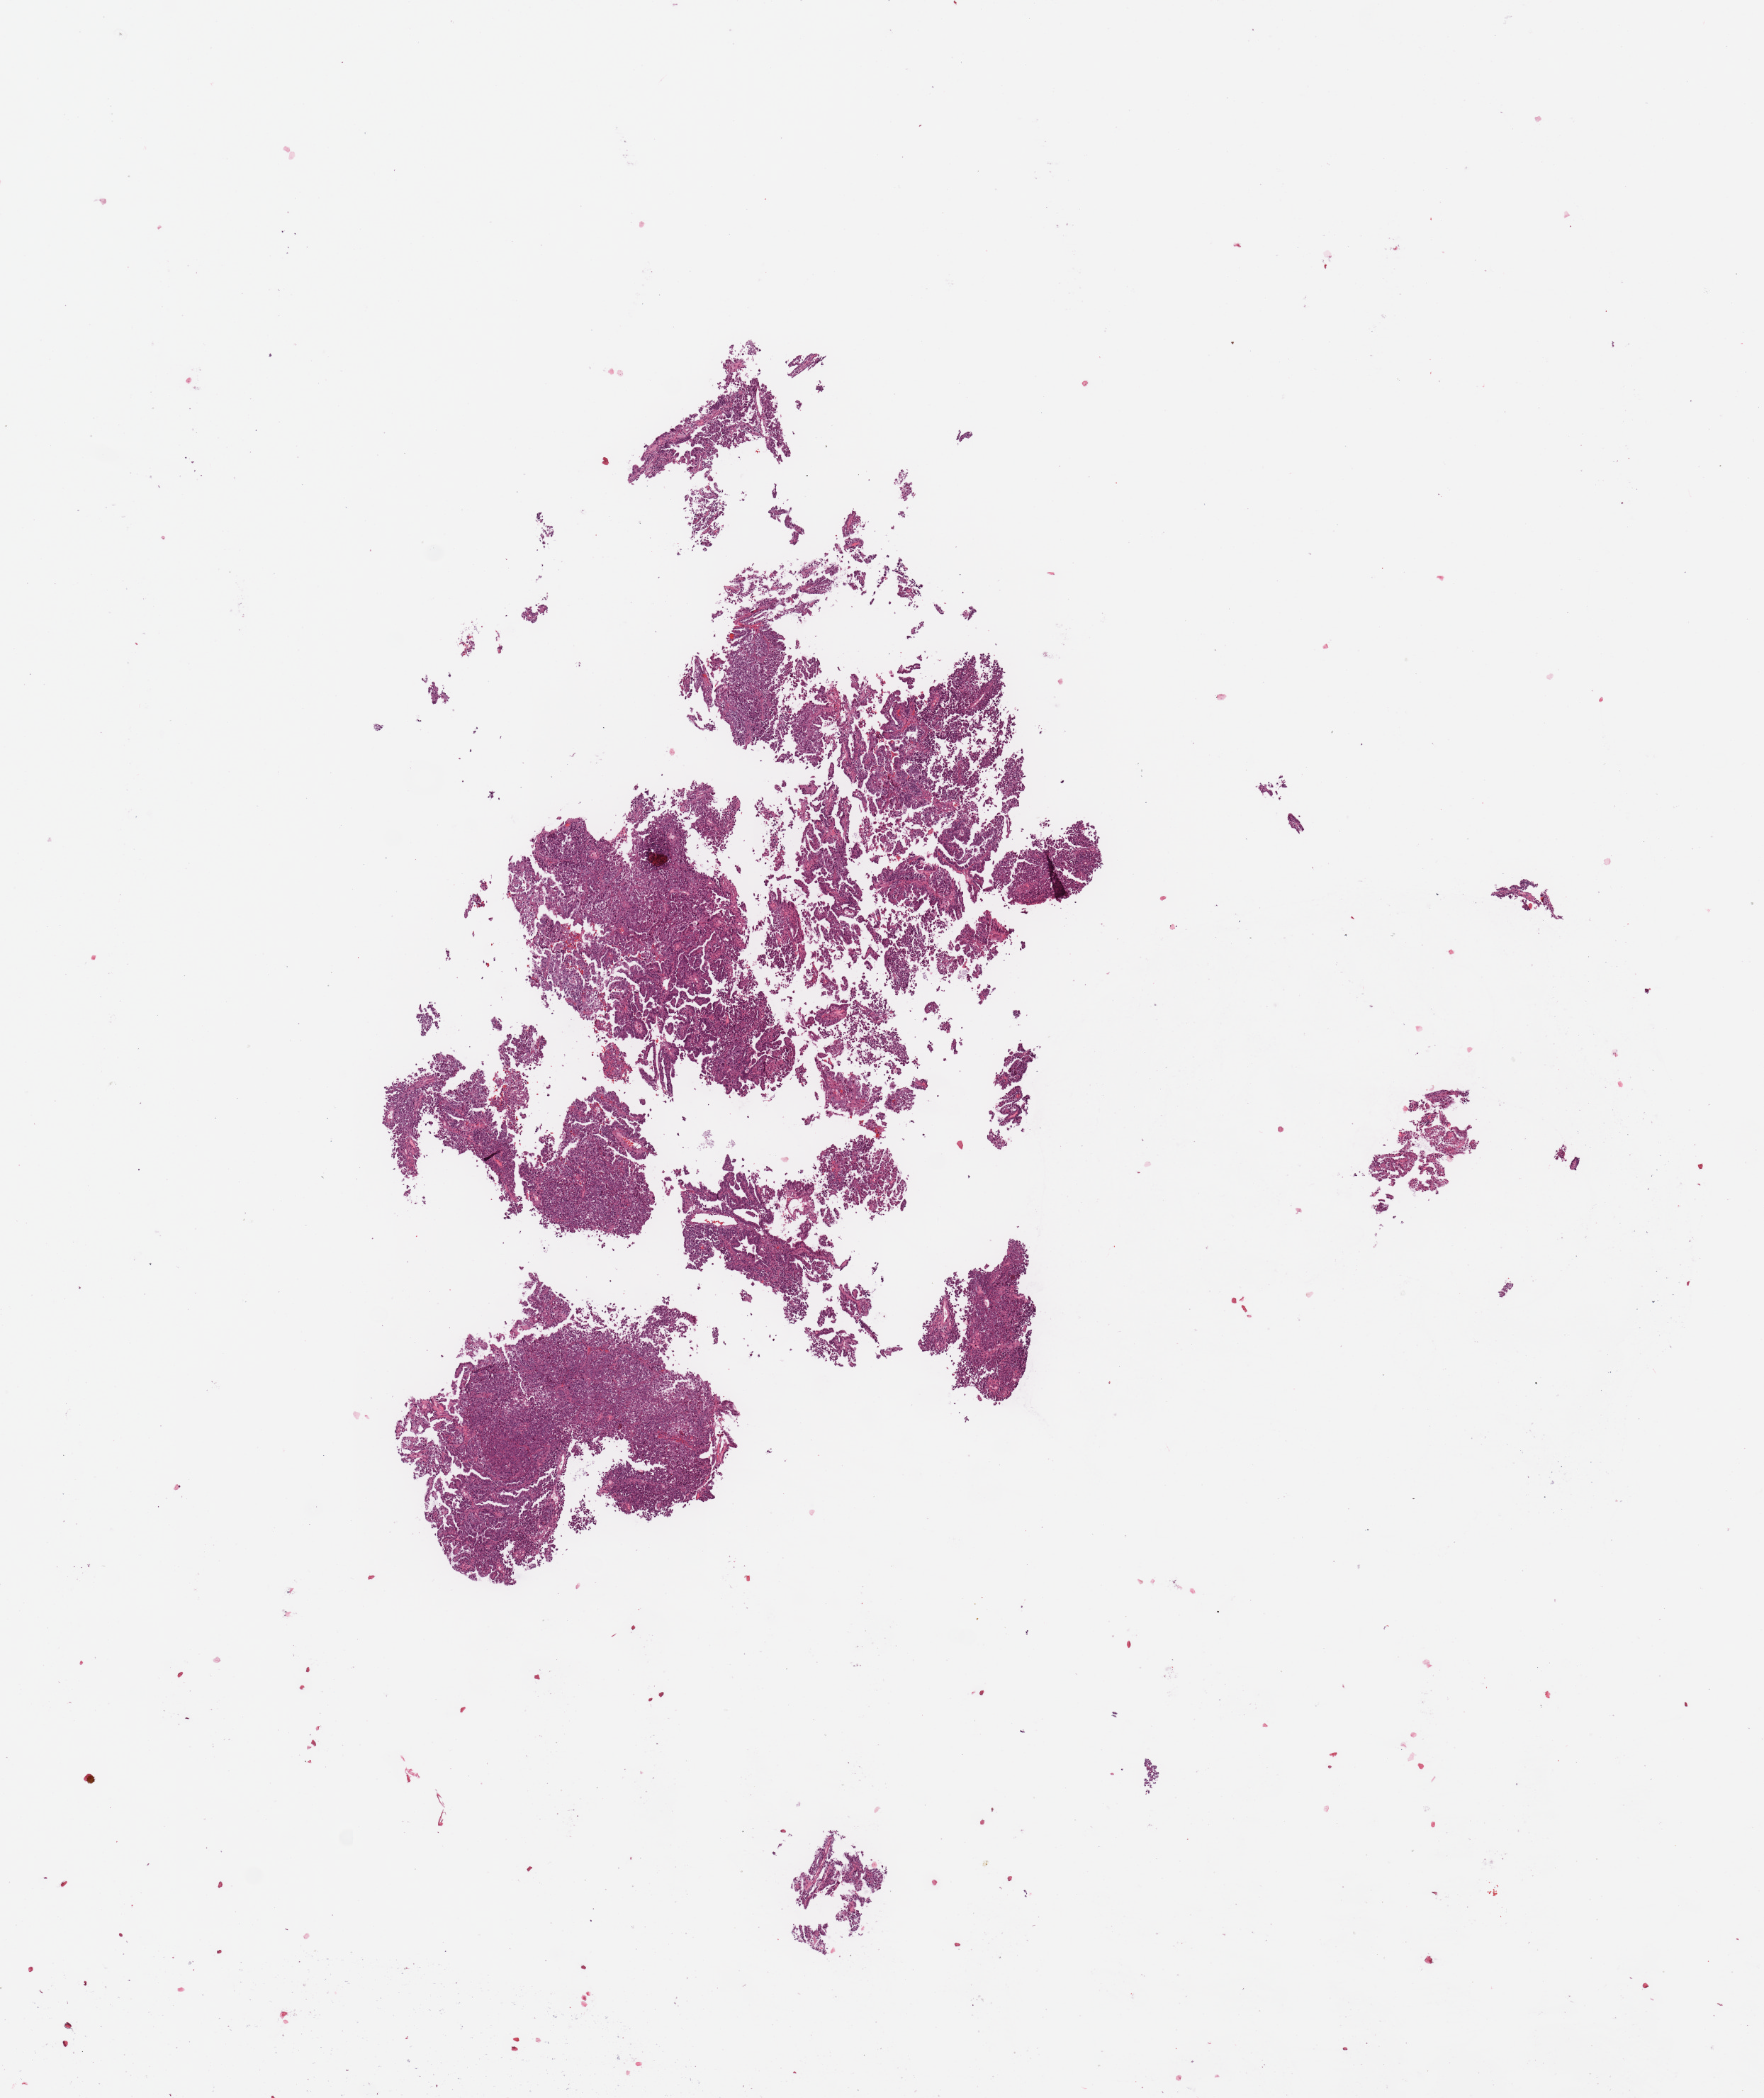
Hematoxylin and eosin (H&E) stained whole-slide image — a low-resolution overview of the entire scanned area, about 9.8 x 11.7 mm (acquisition: 20x scan). Tumour tissue sample, uterus. 73-year-old female patient. Histologic grade: G2 (moderately differentiated).
Histologic diagnosis: Endometrioid adenocarcinoma, NOS. AJCC pathologic stage: IB. Primary tumour site (as recorded): posterior endometrium.